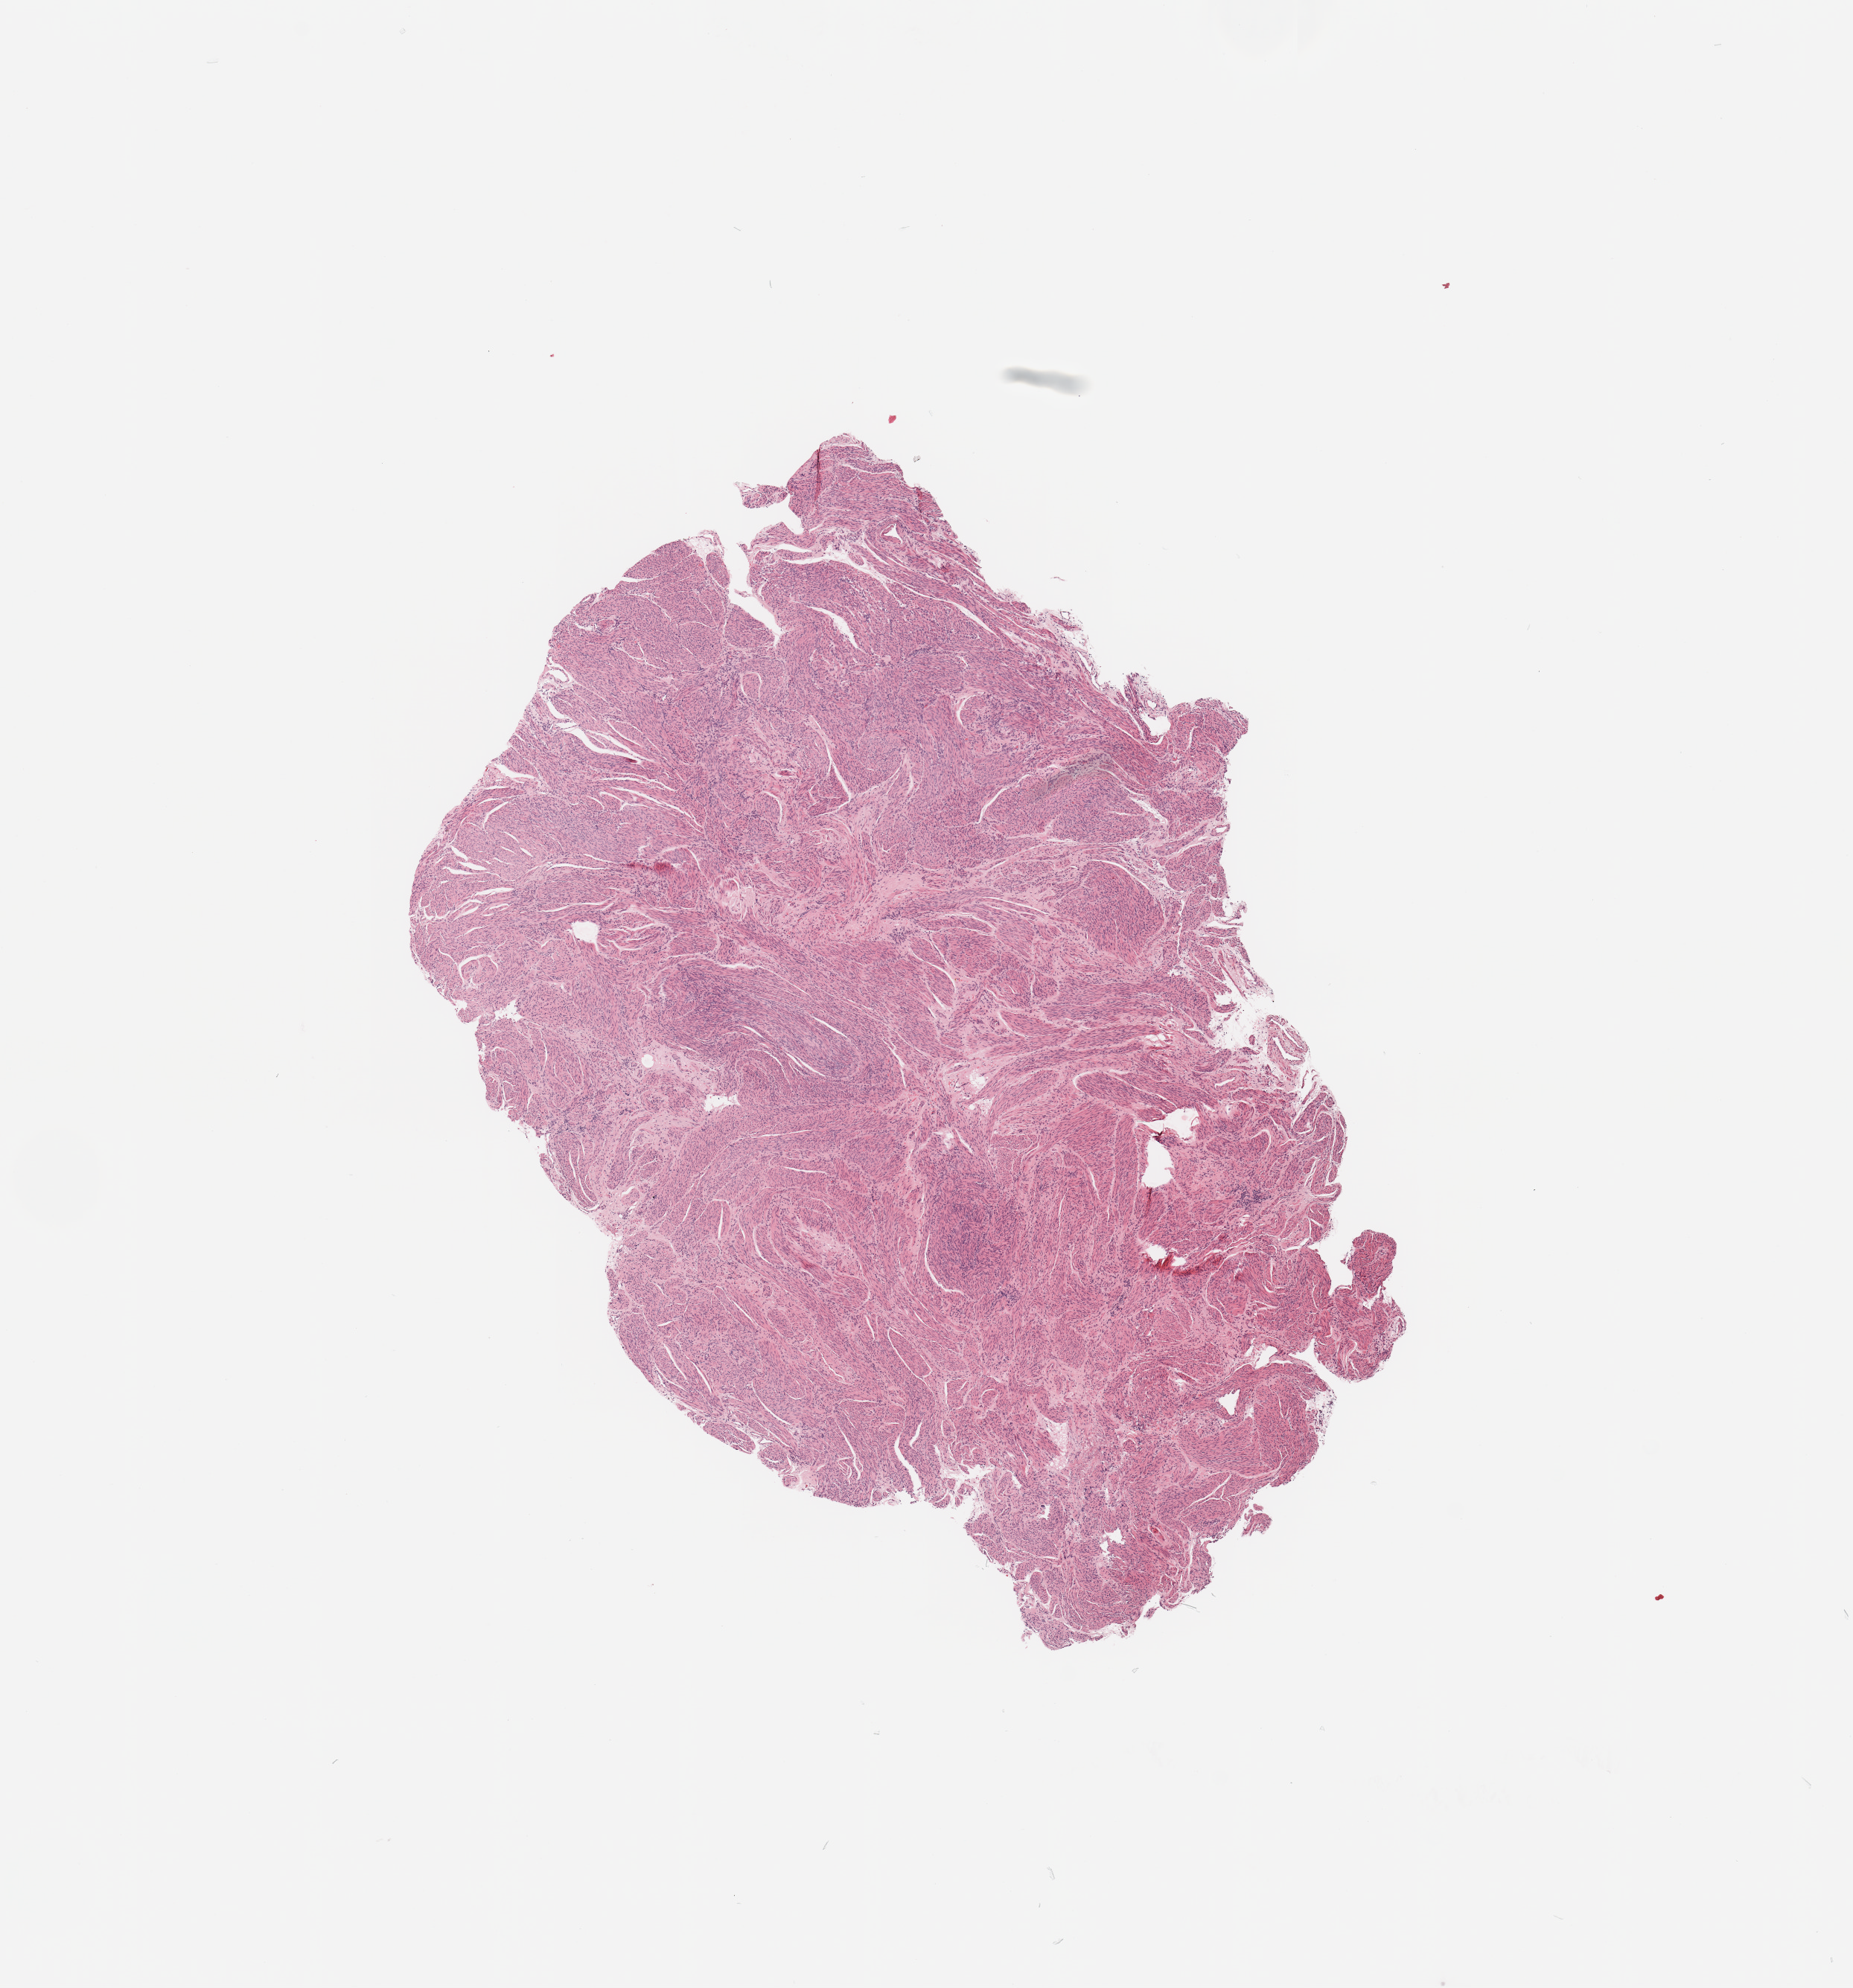
Whole-slide histology image, Hematoxylin and eosin (H&E) stained, a low-resolution overview of the entire scanned area, about 9.8 x 10.6 mm; normal (non-tumour) tissue sample, uterus. Patient: female, age 64 years.
- this section: normal (non-tumour) tissue from the same patient
- patient diagnosis: Endometrioid adenocarcinoma, NOS